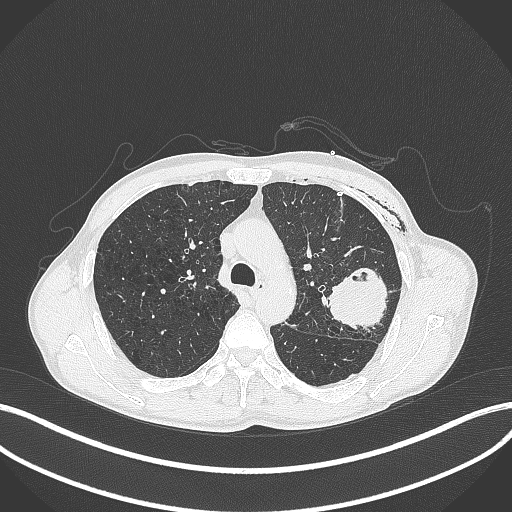
Chest CT, one axial slice; slice 282 of 457 in the series (ordered by position); reconstruction kernel B70f; lung window (W 1500 / L -600 HU); 512 × 512 image matrix, field of view 400 × 400 mm. Patient: male, 58 years. Case-level facts recorded for this patient, not image findings: clinical TNM (as recorded): T3 N0 M0.
Annotated regions visible in this slice (rectangle marked by the reading radiologist):
- lung tumour (recorded histology: adenocarcinoma): box from (x=323, y=264) to (x=389, y=334) px